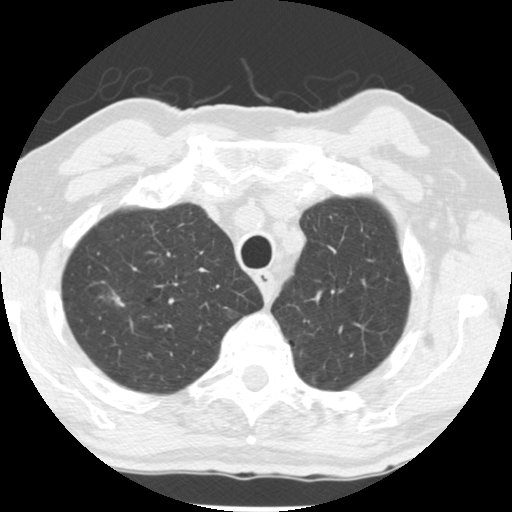
Low-dose screening chest CT, one axial slice; position 210 of 252 along the scan axis; reconstruction kernel STANDARD; lung window (W 1500 / L -600 HU); 2.5 mm slice thickness; 512 × 512 image matrix.
Structures marked on this image (manually delineated by an expert):
- lesion 1 (tumor, upper lobe of right lung): bounding box (x1, y1, x2, y2) in pixels: (101, 291, 125, 307)